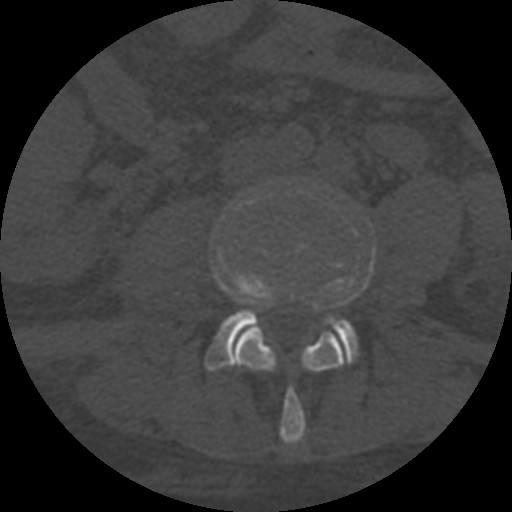
CT including the spine, one axial slice; slice 221 of 708 in the series (ordered by position); reconstruction kernel STANDARD; 120 kVp; one of 3 acquisitions stored at this slice position; bone window (W 1800 / L 400 HU); 1.25 mm slice thickness; 512 × 512 image matrix. Patient age 55 years. Case-level facts recorded for this patient, not image findings: primary cancer: colon; vertebrae with lytic lesions (as recorded): T12, L1, L5.
Outlined on this slice (semi-automatic segmentation, software-assisted and operator-edited):
- L3 vertebra: bounding box <233,327,345,444> (left, top, right, bottom; pixels)
- L4 vertebra: <204,201,375,370>